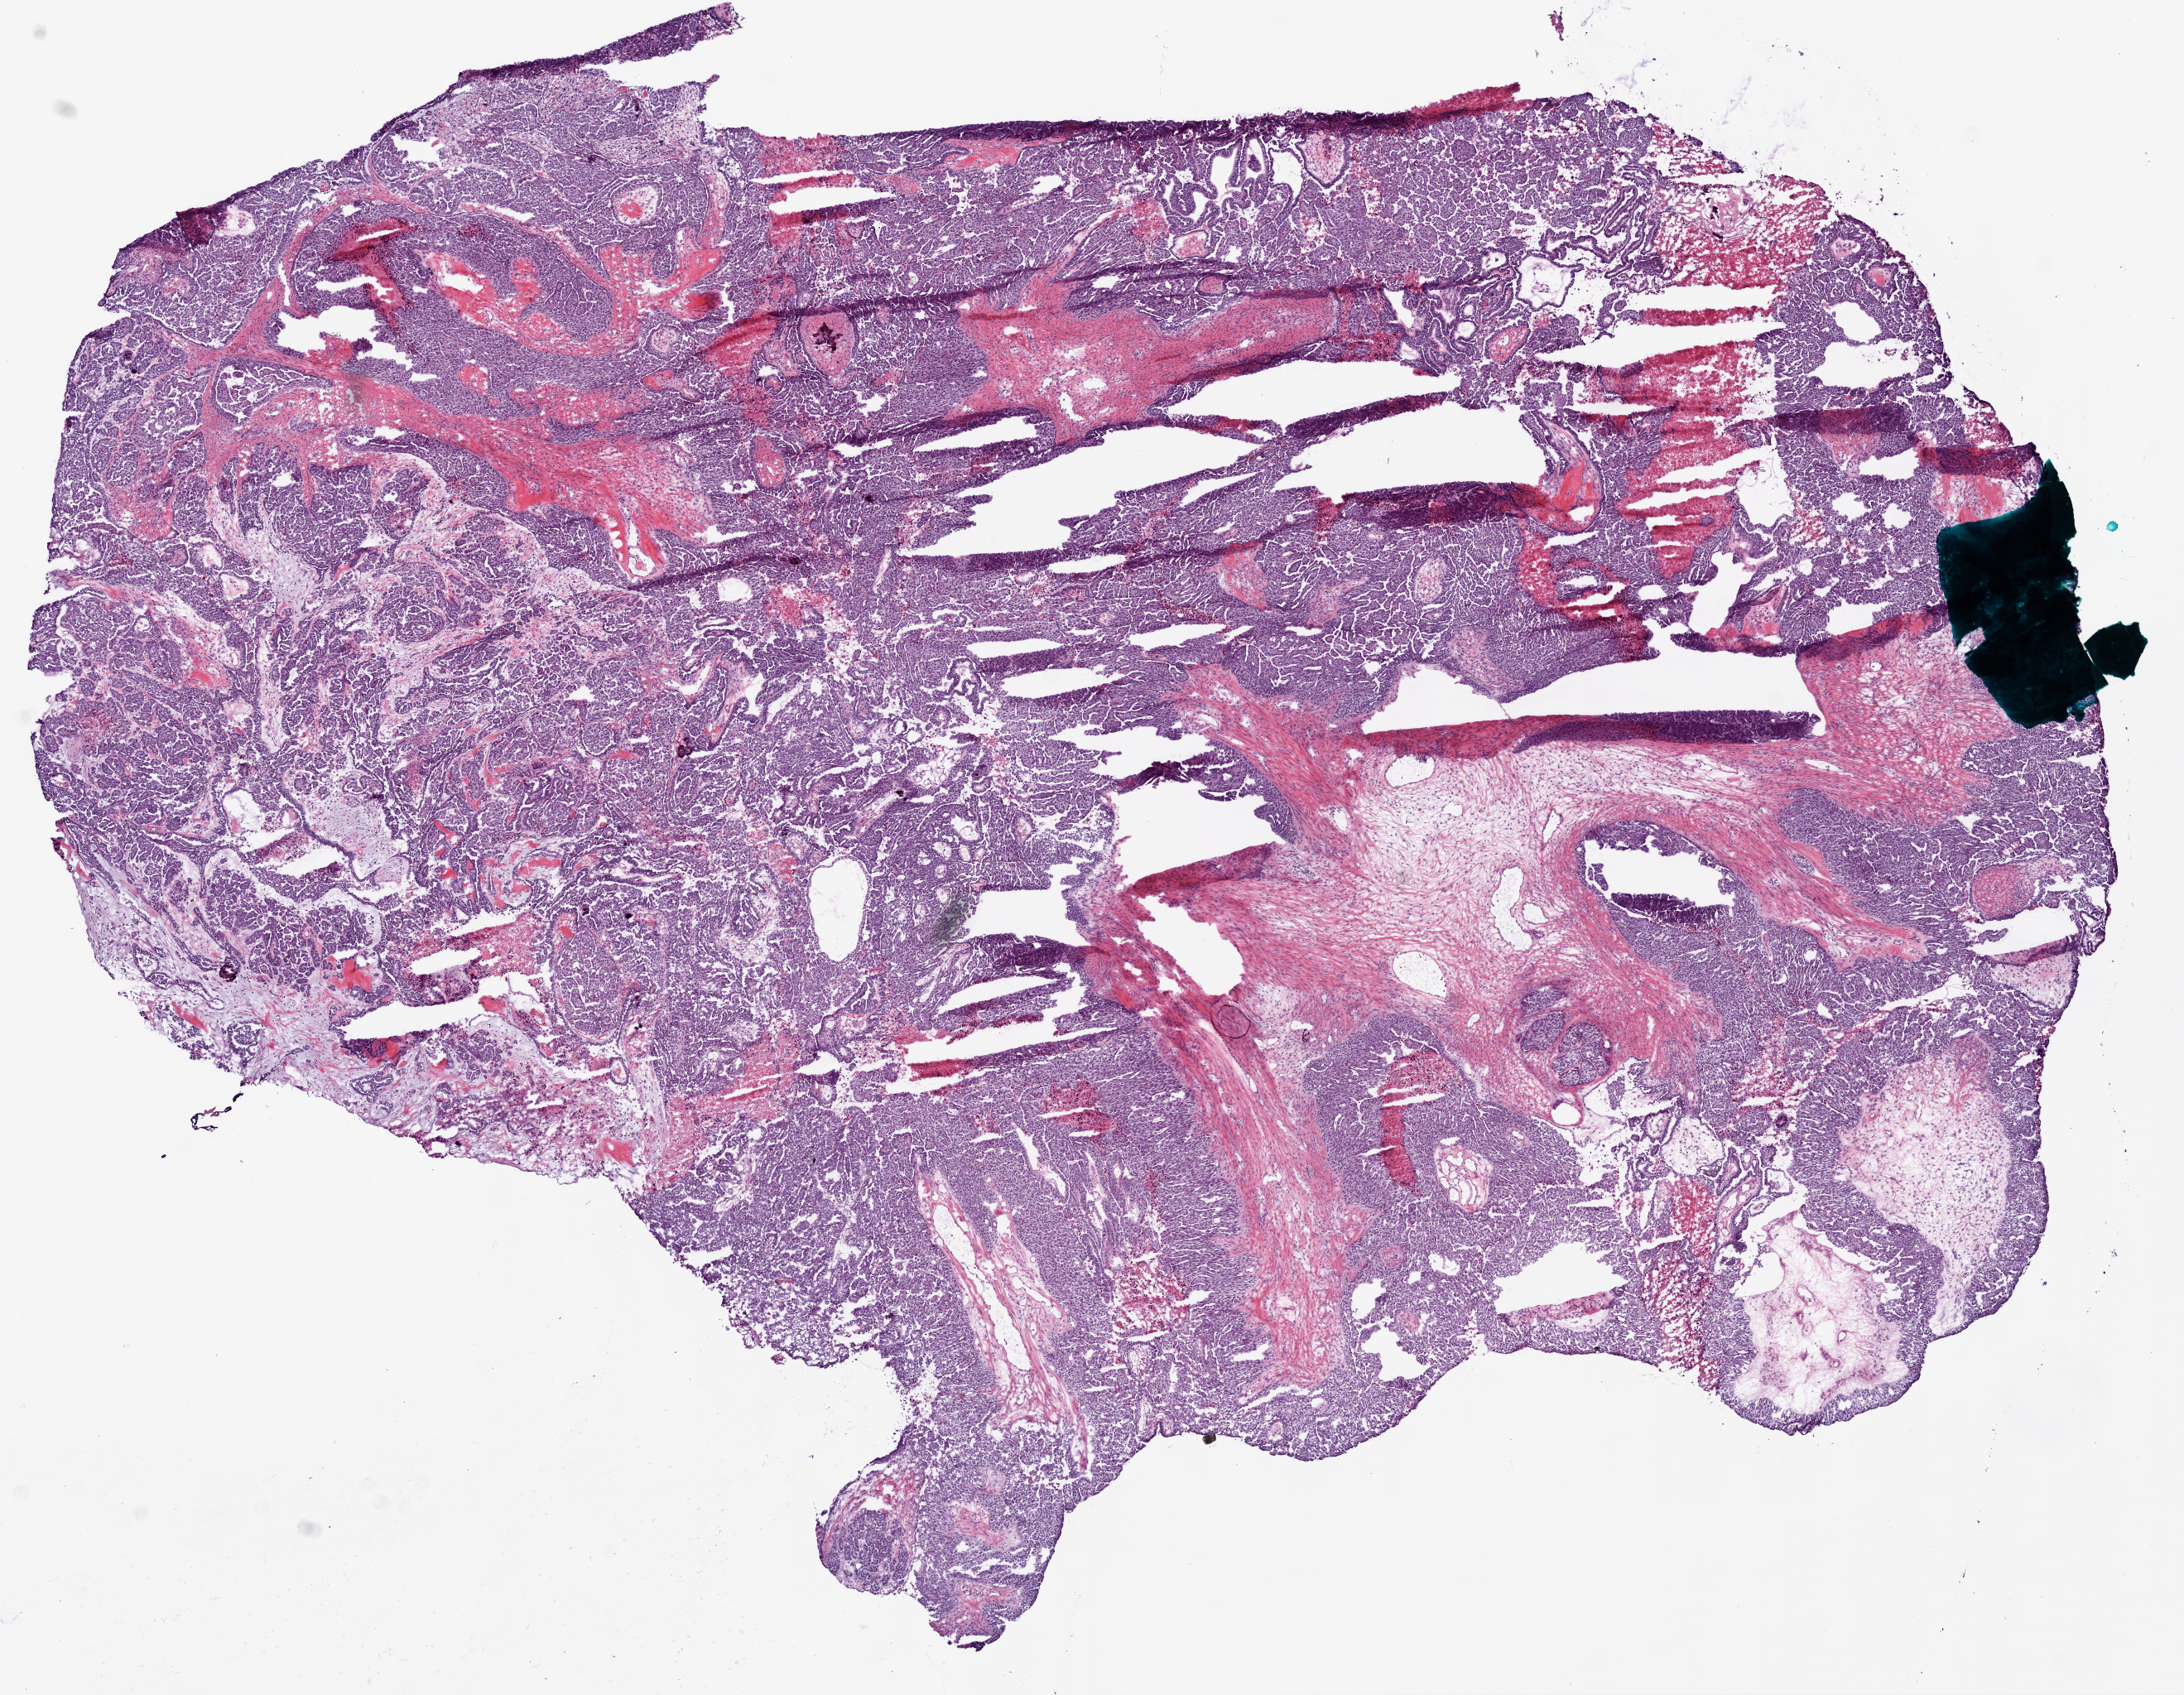
Digitized Hematoxylin and eosin (H&E) stained tissue section (whole slide) — shown as a low-resolution overview of the whole scanned area (about 10.6 x 8.3 mm). Frozen section from the bottom of the tissue portion. Ovary, primary tumour sample. Female, age 66 years at initial diagnosis. Histologic grade: G3 (poorly differentiated). Composition of this section per pathologist review: tumour cells 70%, tumour nuclei 90%, normal cells 0%, stromal cells 30%, necrosis 0%.
FIGO stage: IIIC. Pathologic diagnosis: Serous cystadenocarcinoma, NOS.